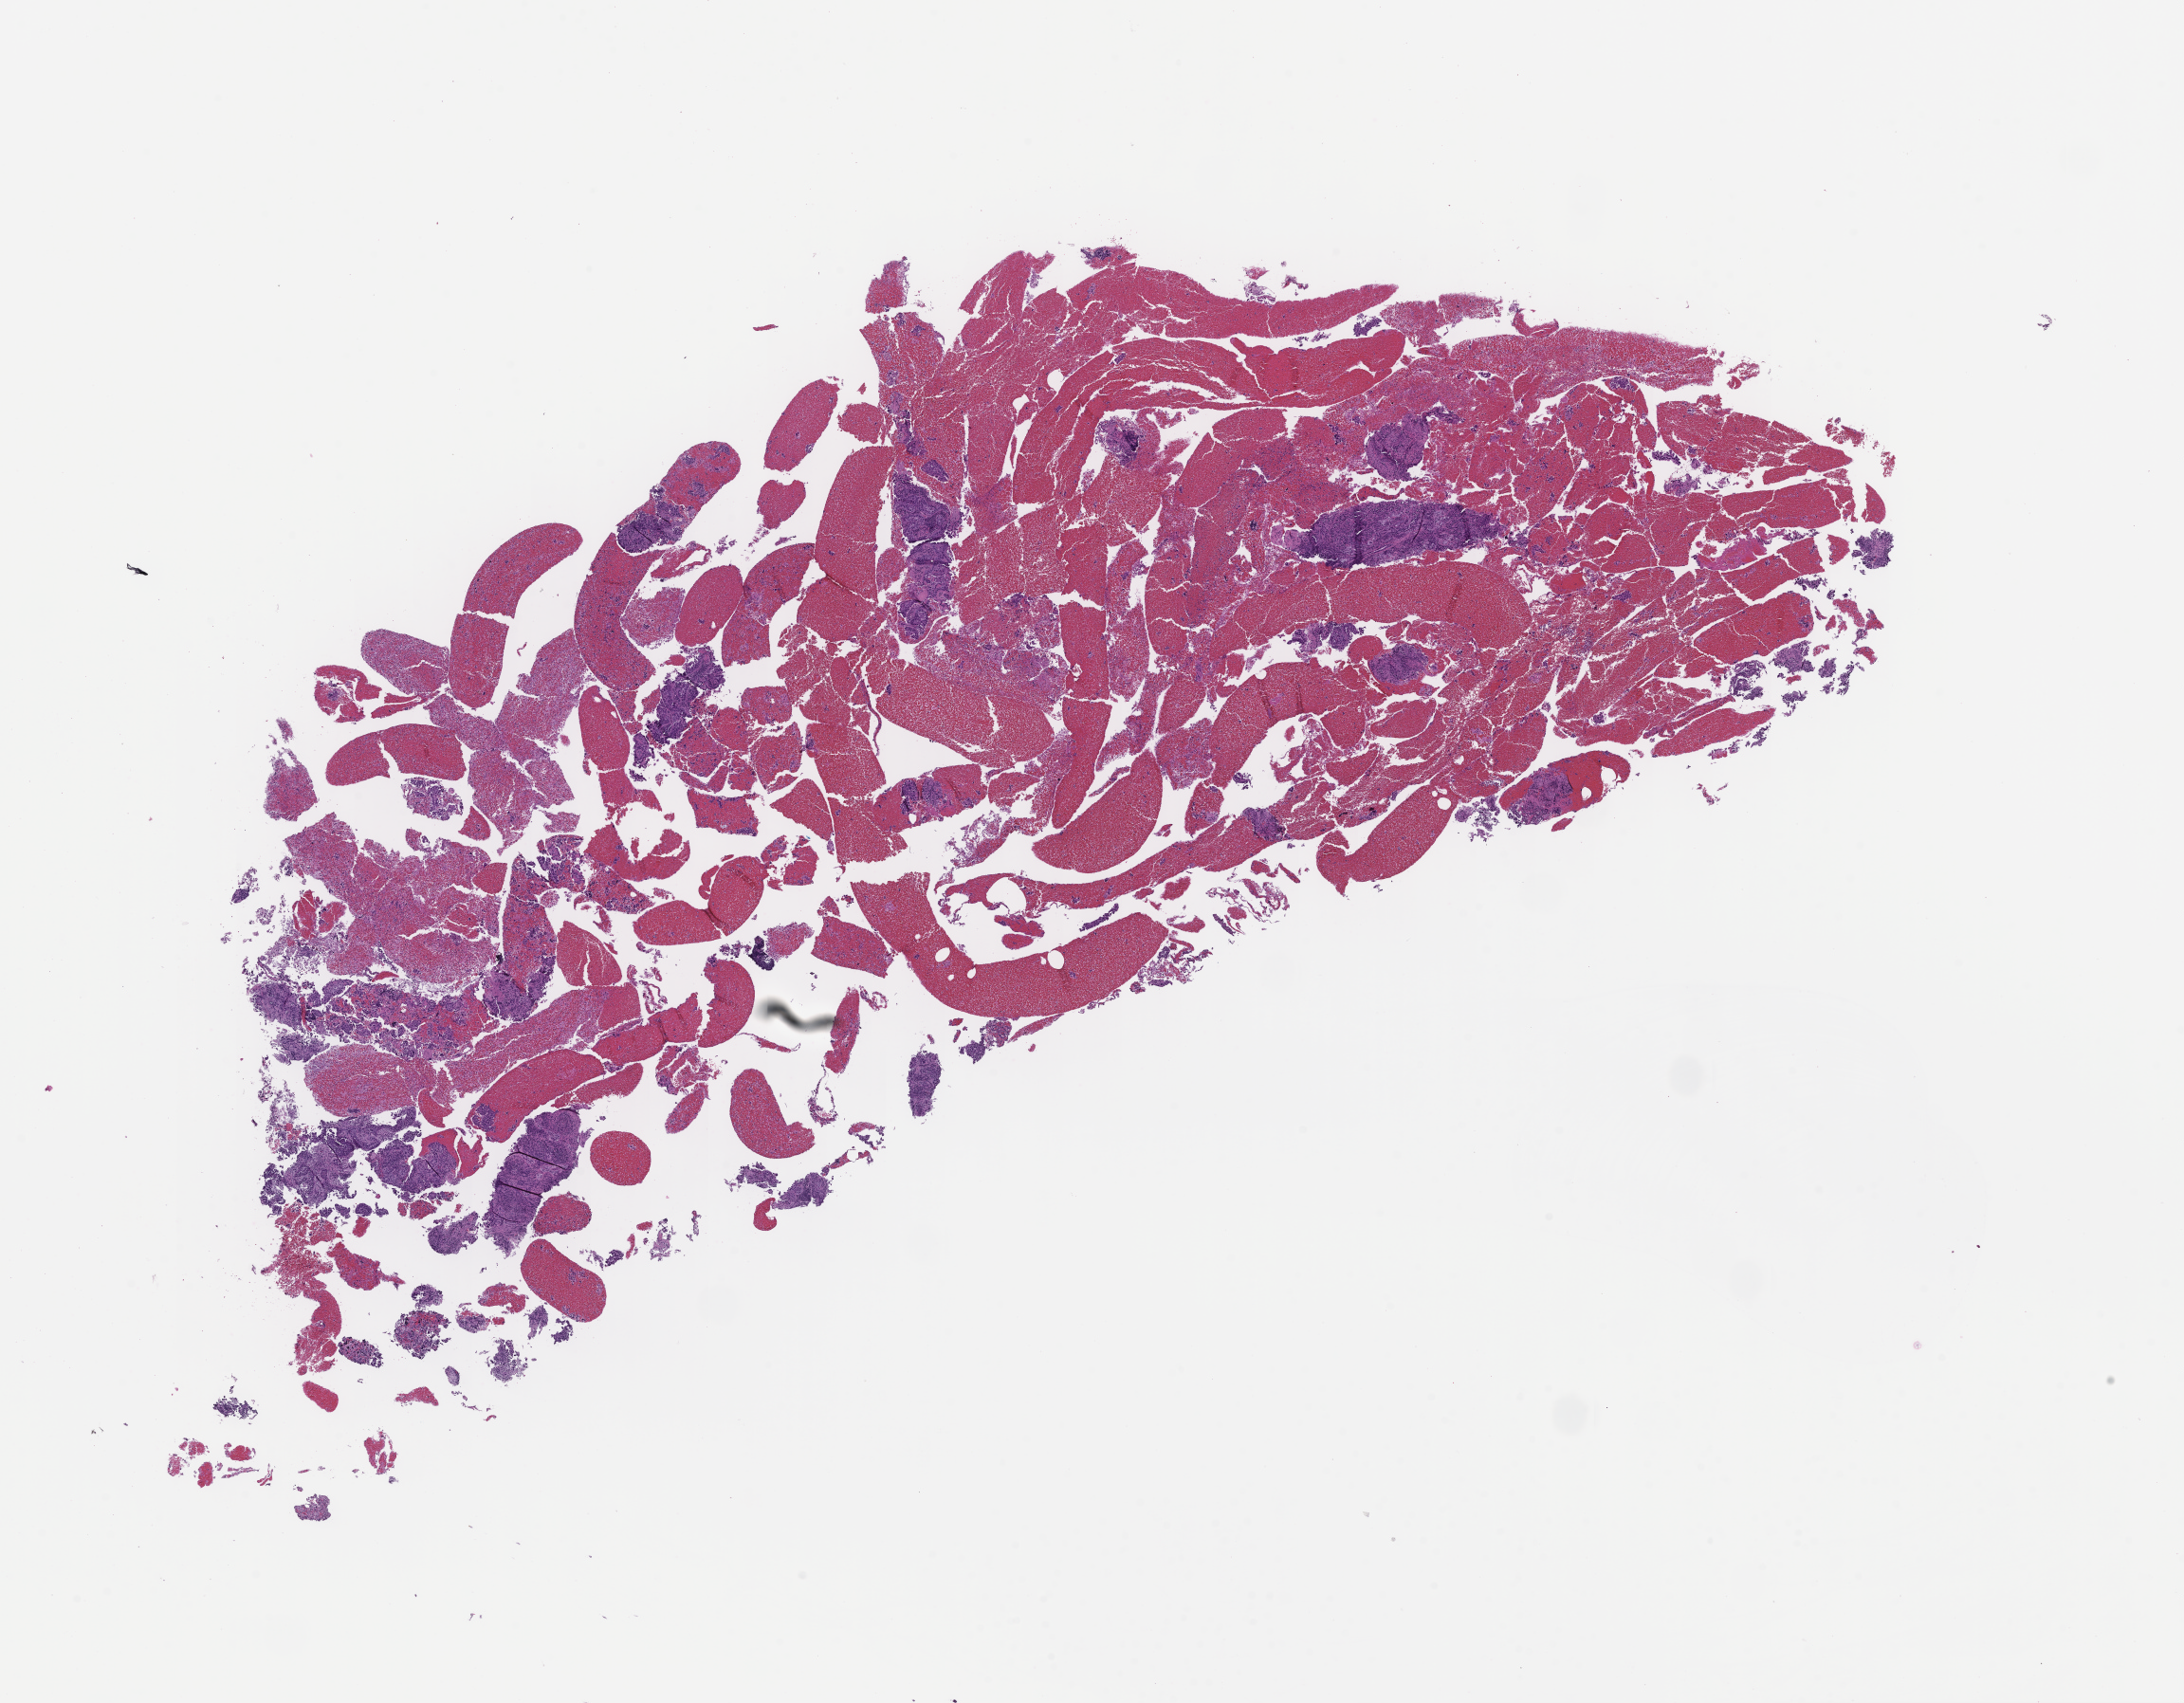
Digitized H&E-stained section, a low-resolution overview of the entire scanned area, about 18.6 x 14.5 mm; formalin-fixed, paraffin-embedded (FFPE) tissue; site: lung. Patient: male.
This section: primary tumour tissue. Diagnosis: Non-Small Cell Lung Carcinoma.